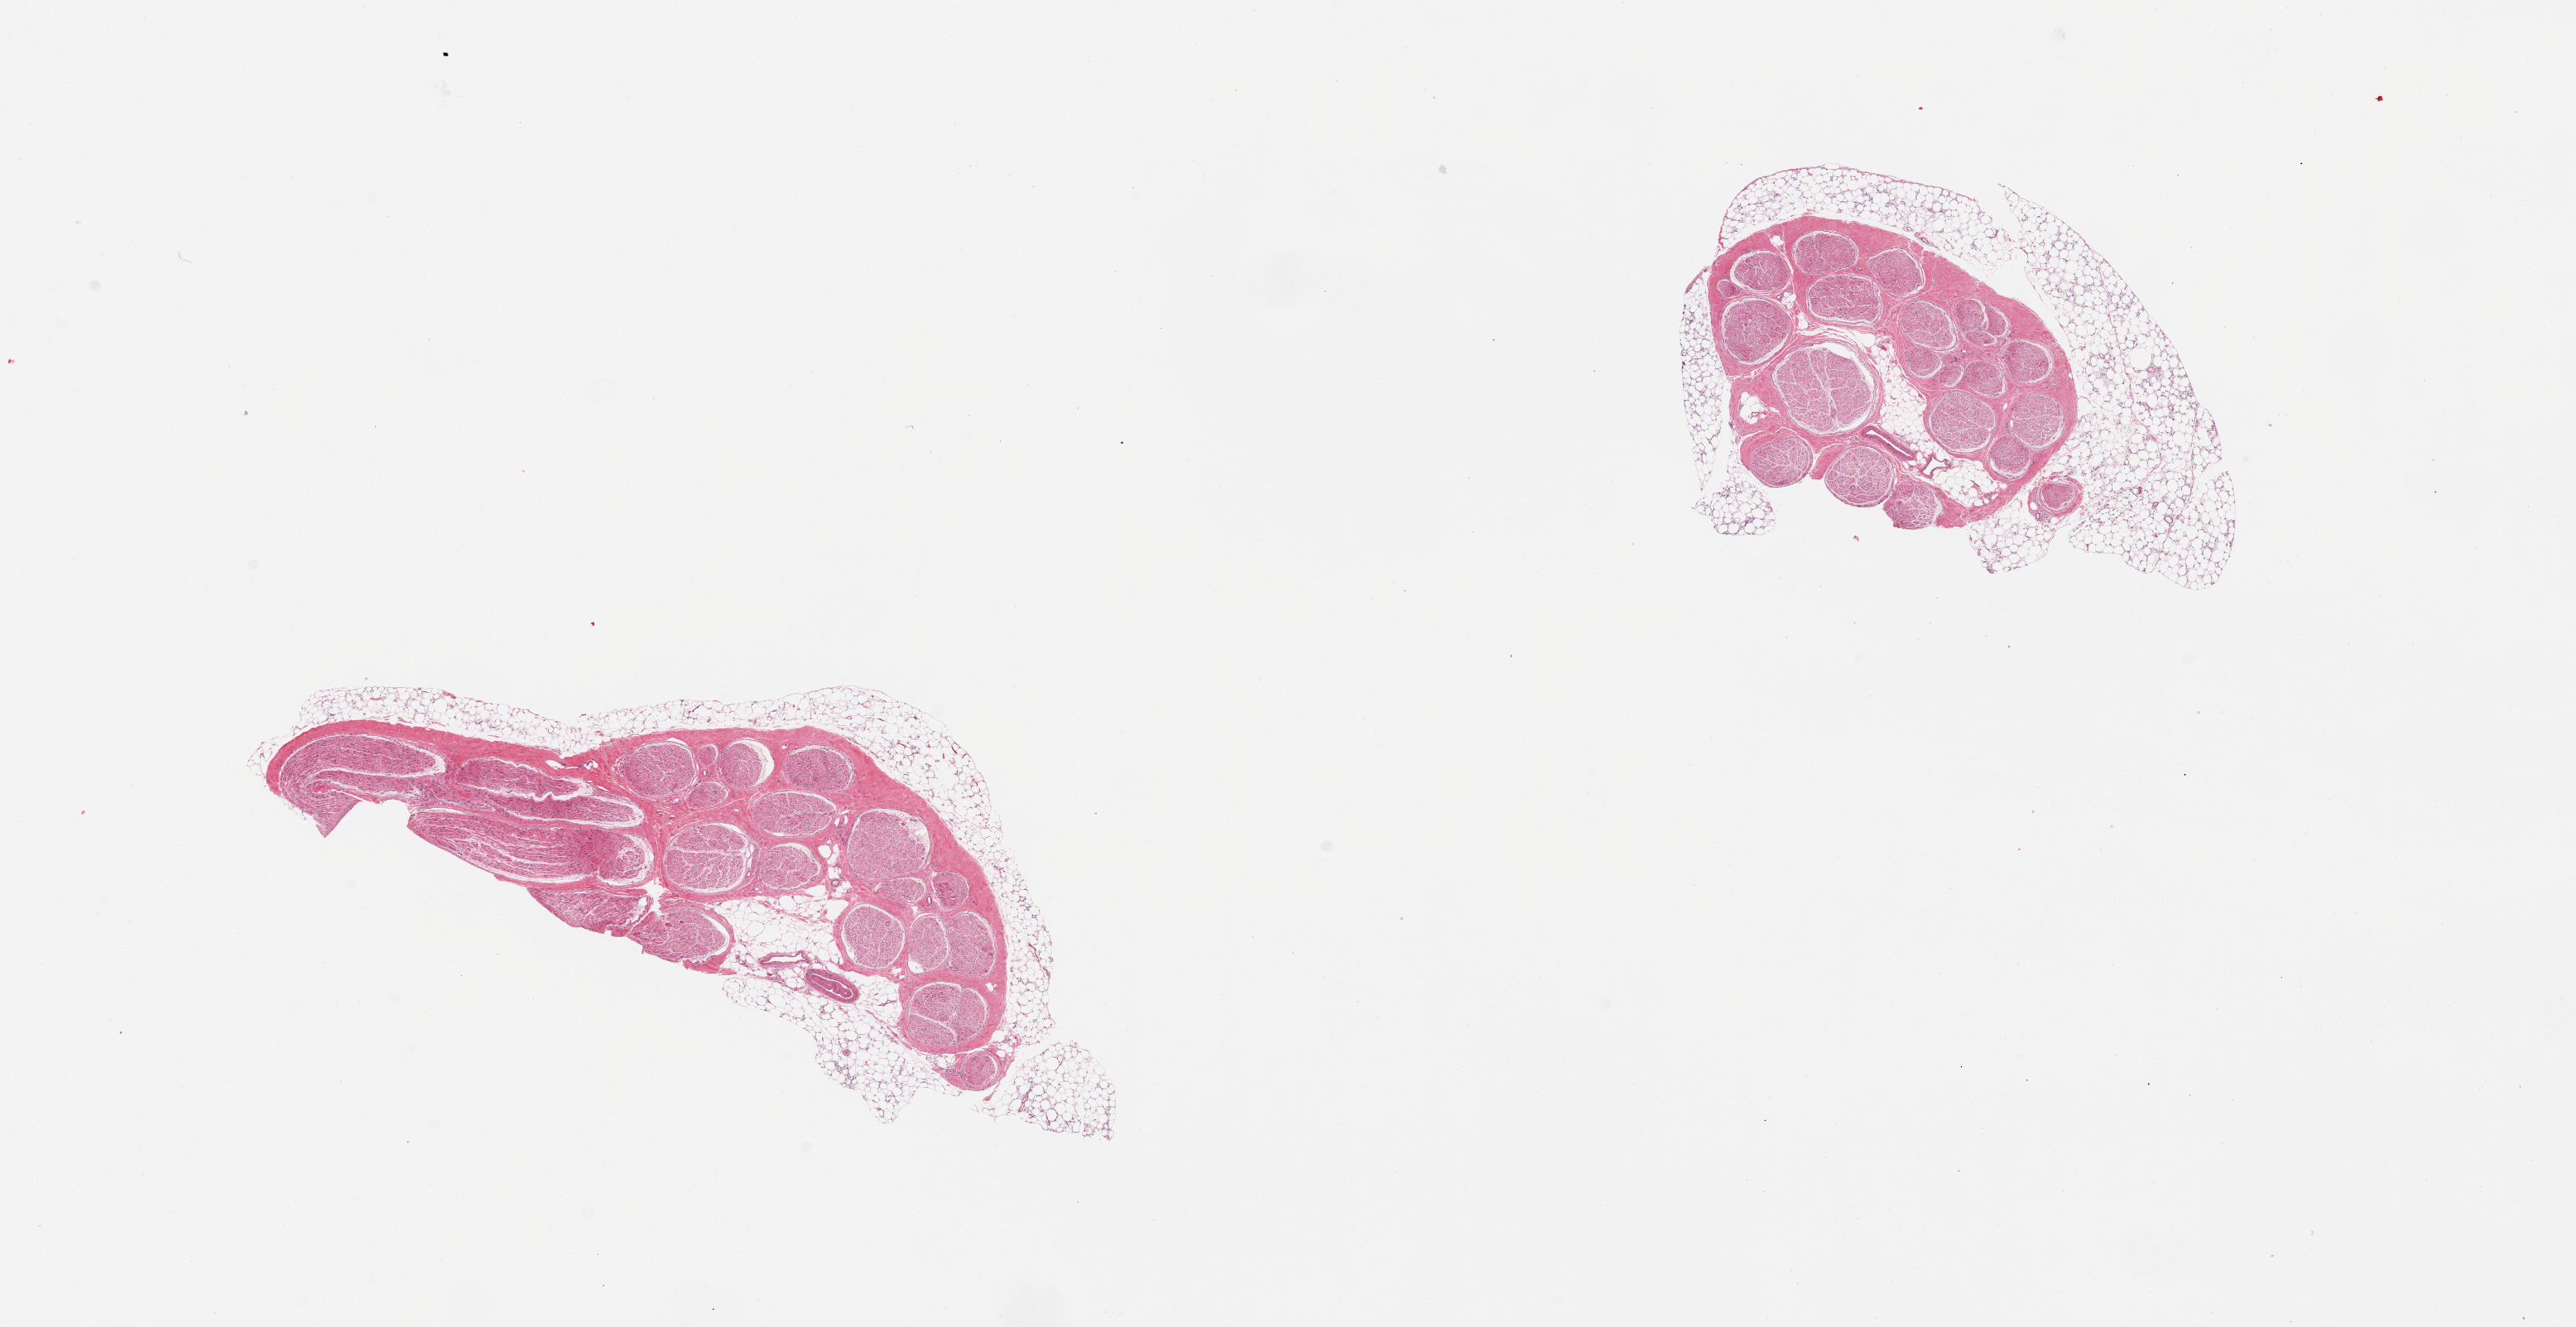
H&E whole-slide image, brightfield — a low-resolution overview of the entire scanned area, about 24.6 x 12.7 mm. PAXgene-fixed paraffin-embedded (PFPE) section. Target tissue: tibial nerve. Donor tissue sample. Donor: male.
Review note (as recorded): 2 pieces; both are partially encased in fat, up to 2mm (20% and 40% internal and external fat combined).